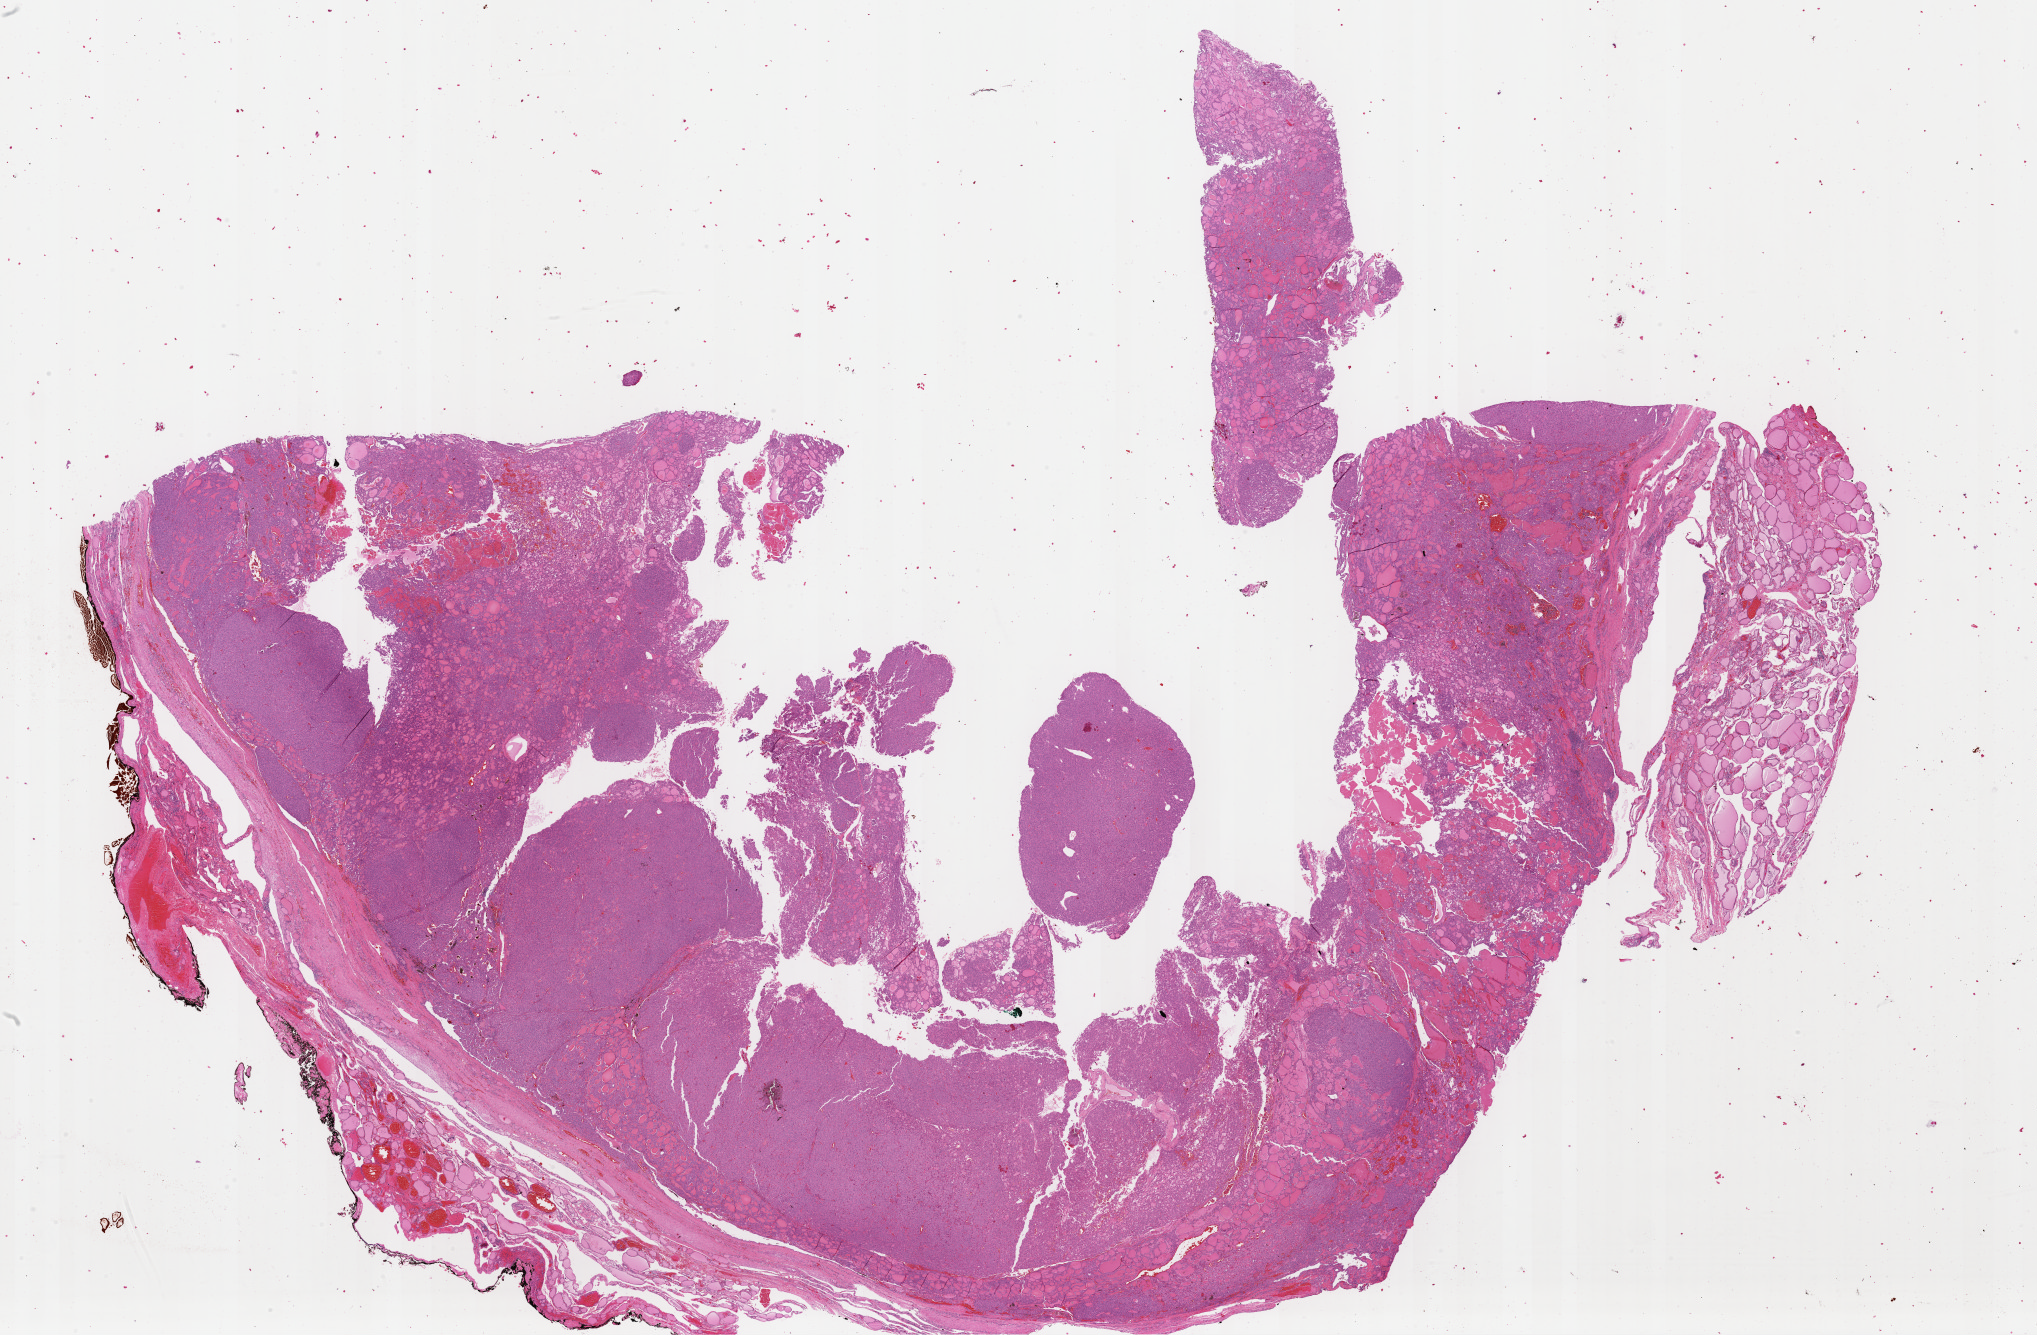
Whole-slide histology image, Hematoxylin and eosin (H&E) stained, a low-resolution overview of the entire scanned area, about 32.2 x 21.1 mm, formalin-fixed paraffin-embedded (FFPE) diagnostic section, primary tumour sample from the thyroid. Female patient; age at initial diagnosis 55 years.
- diagnosis: Papillary carcinoma, follicular variant (thyroid gland)
- lymph nodes positive (case pathology): 0 of 2 examined
- AJCC pathologic stage: III (6th edition)